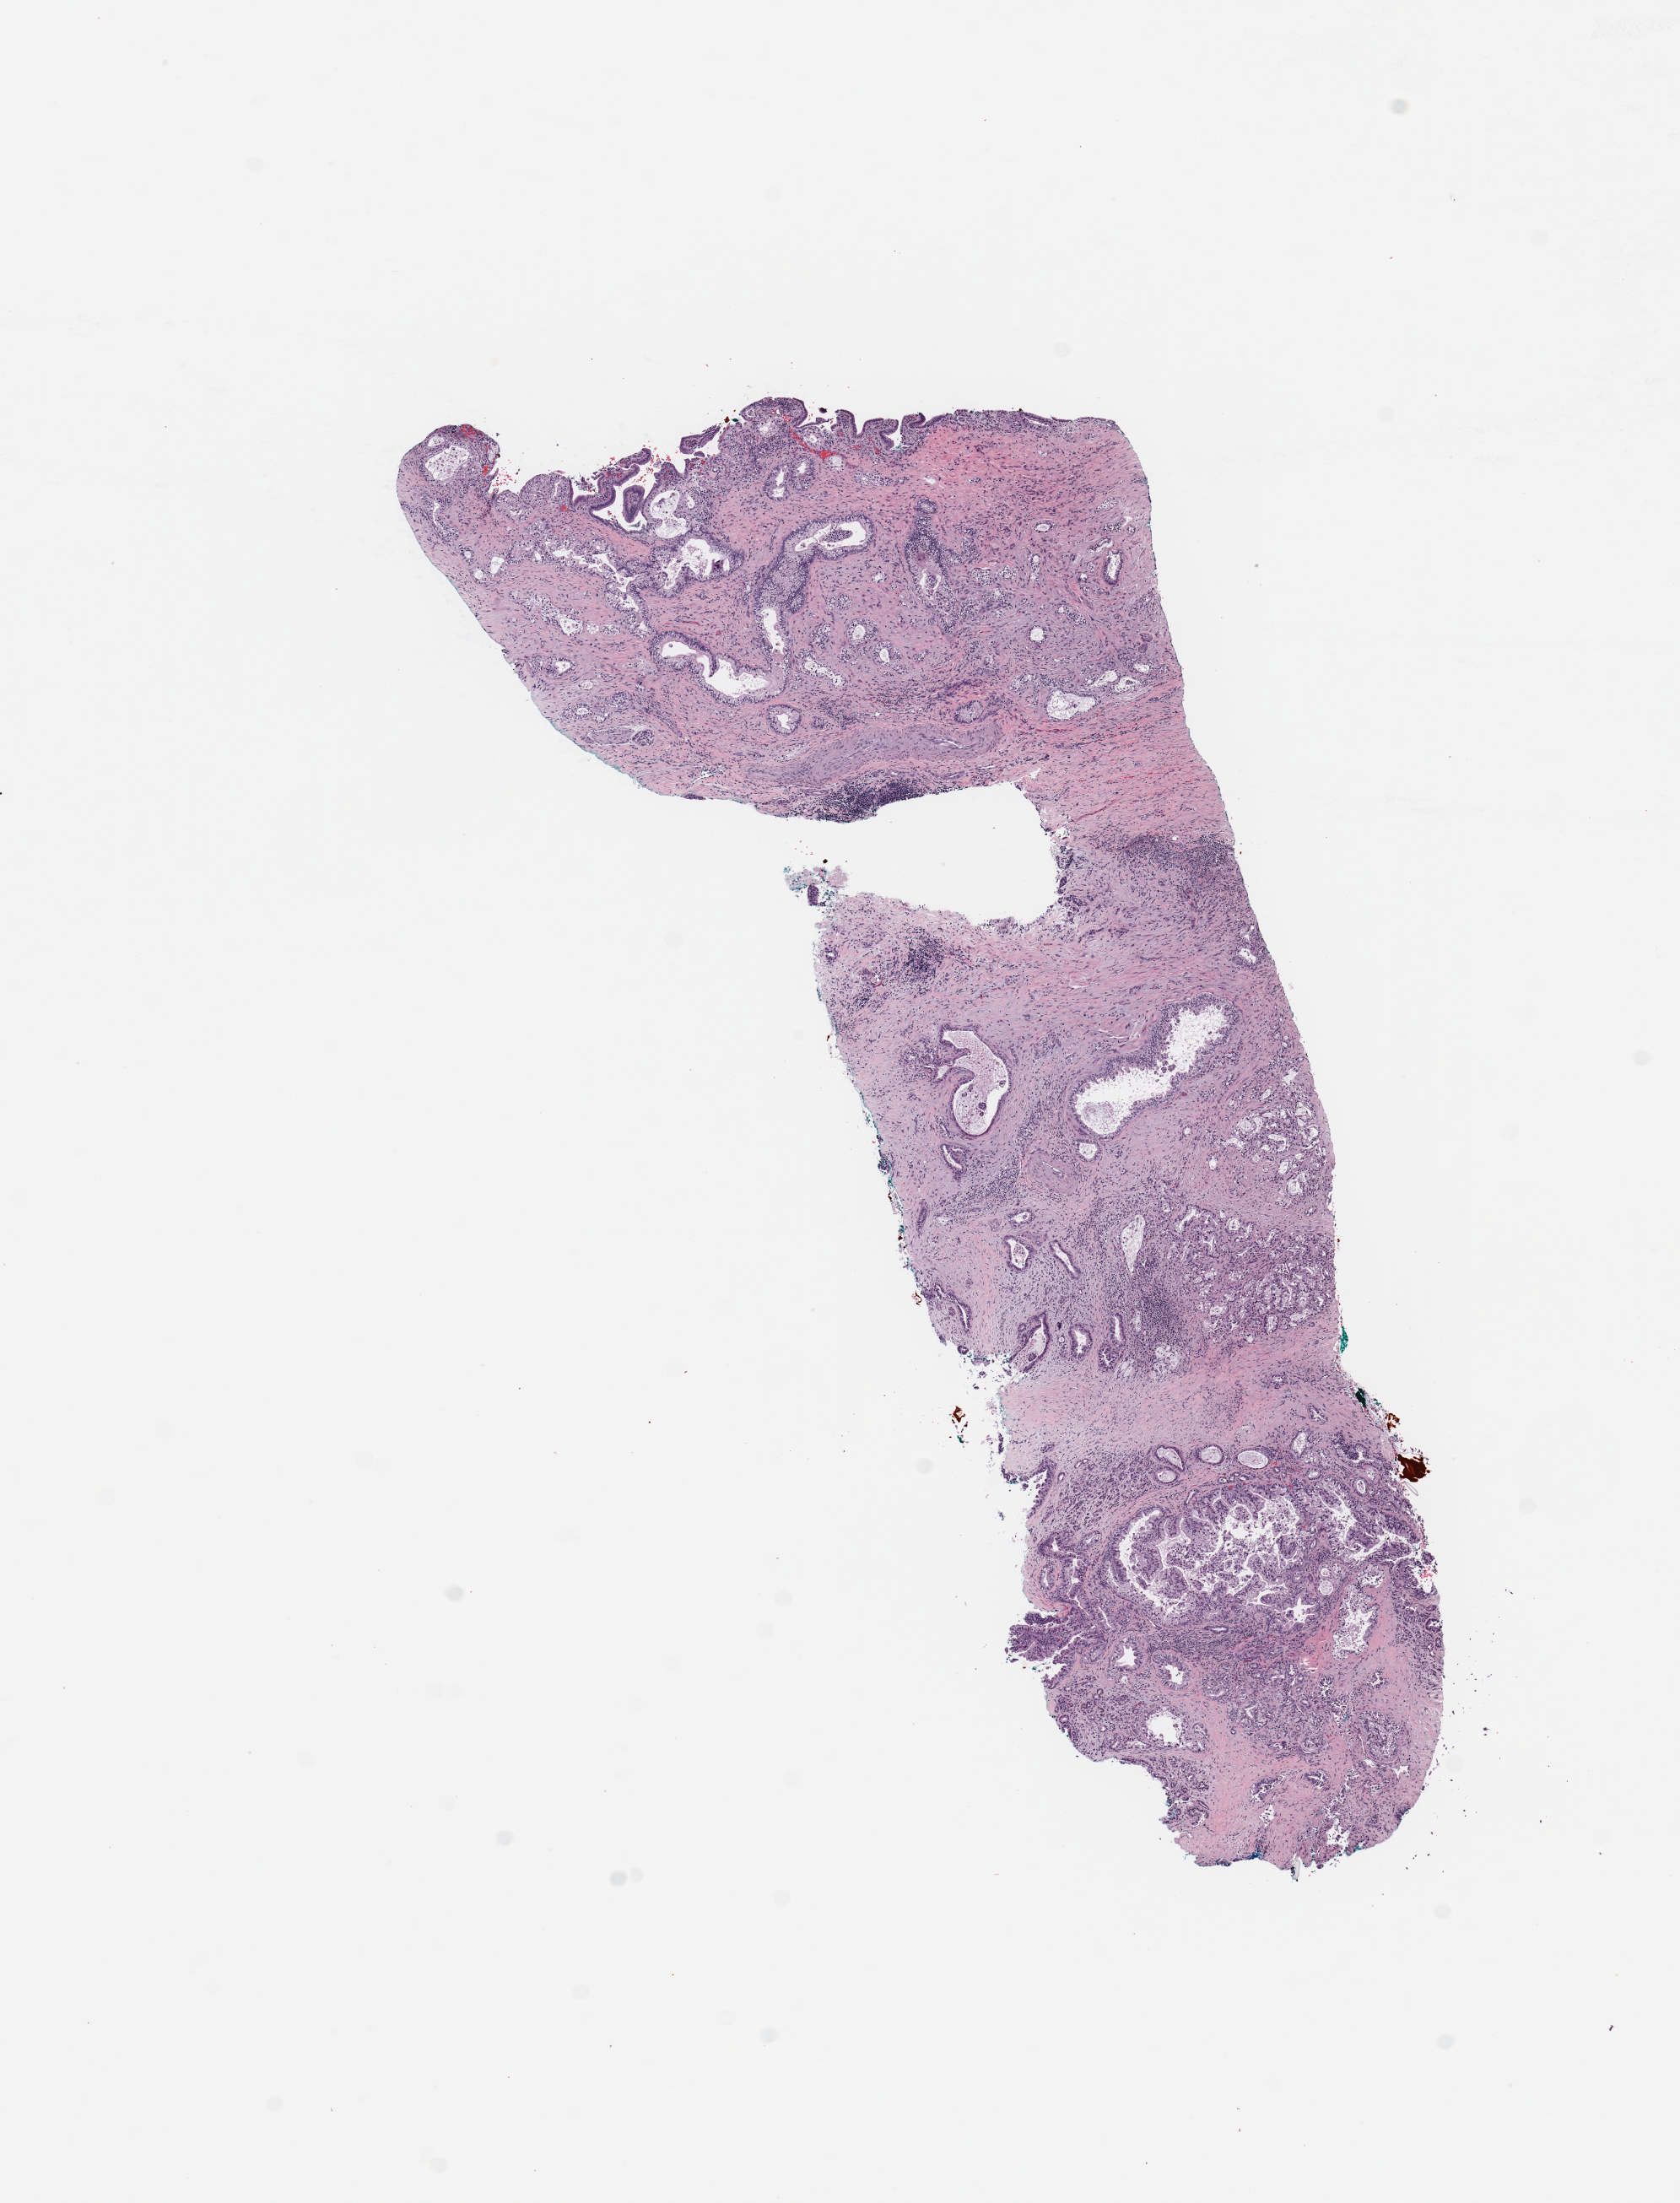
Whole-slide histology image, H&E-stained, shown as a low-resolution overview of the whole scanned area (about 7.9 x 10.3 mm); pancreas, tumour tissue. Male, 70 y/o. Histologic grade: G3 (poorly differentiated).
• AJCC pathologic stage: IIB
• primary tumour site (as recorded): head
• histologic diagnosis: Infiltrating duct carcinoma, NOS